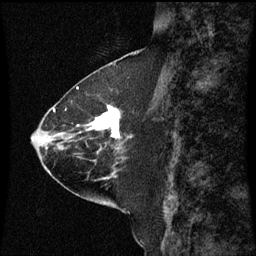
Breast MRI (dynamic contrast-enhanced), one sagittal slice; slice 26 of 60 in the series (ordered by position); dynamic contrast-enhanced series, image 2 of 3 at this slice position (ordered by acquisition); 1.5 T; TE 4.2 ms, TR 8.9 ms; 256 × 256 image matrix, field of view 200 × 200 mm. Patient: female, 63 years. From the clinical record (not read from this slice): setting: breast cancer imaged before/during neoadjuvant chemotherapy; receptor status: HR-positive, HER2-negative.
Structures marked on this image (semi-automatic segmentation, software-assisted and operator-edited):
- analysis volume of interest (the breast-tissue region the enhancement analysis was run in; not a lesion): bounding box <77,104,131,151> (left, top, right, bottom; pixels)
- tumour enhancement mask (voxels above the 70 % enhancement threshold inside the analysis volume of interest): <89,106,120,139>